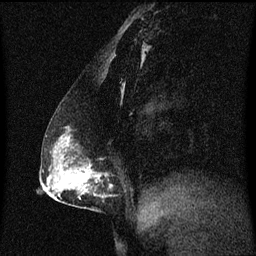
Breast MRI (dynamic contrast-enhanced), one sagittal slice. Slice 33 of 60 in the series (ordered by position). Dynamic contrast-enhanced series, image 2 of 3 at this slice position (ordered by acquisition). 1.5 T. TE 4.2 ms, TR 8.4 ms. 256 × 256 image matrix, field of view 200 × 200 mm. Female patient, age 40 years. From the clinical record (not read from this slice): setting: breast cancer imaged before/during neoadjuvant chemotherapy; receptor status: triple-negative.
Annotated regions visible in this slice (semi-automatic segmentation, software-assisted and operator-edited):
- analysis volume of interest (the breast-tissue region the enhancement analysis was run in; not a lesion): box from (x=58, y=126) to (x=113, y=211) px
- tumour enhancement mask (voxels above the 70 % enhancement threshold inside the analysis volume of interest): (x=66, y=138)–(x=91, y=191)